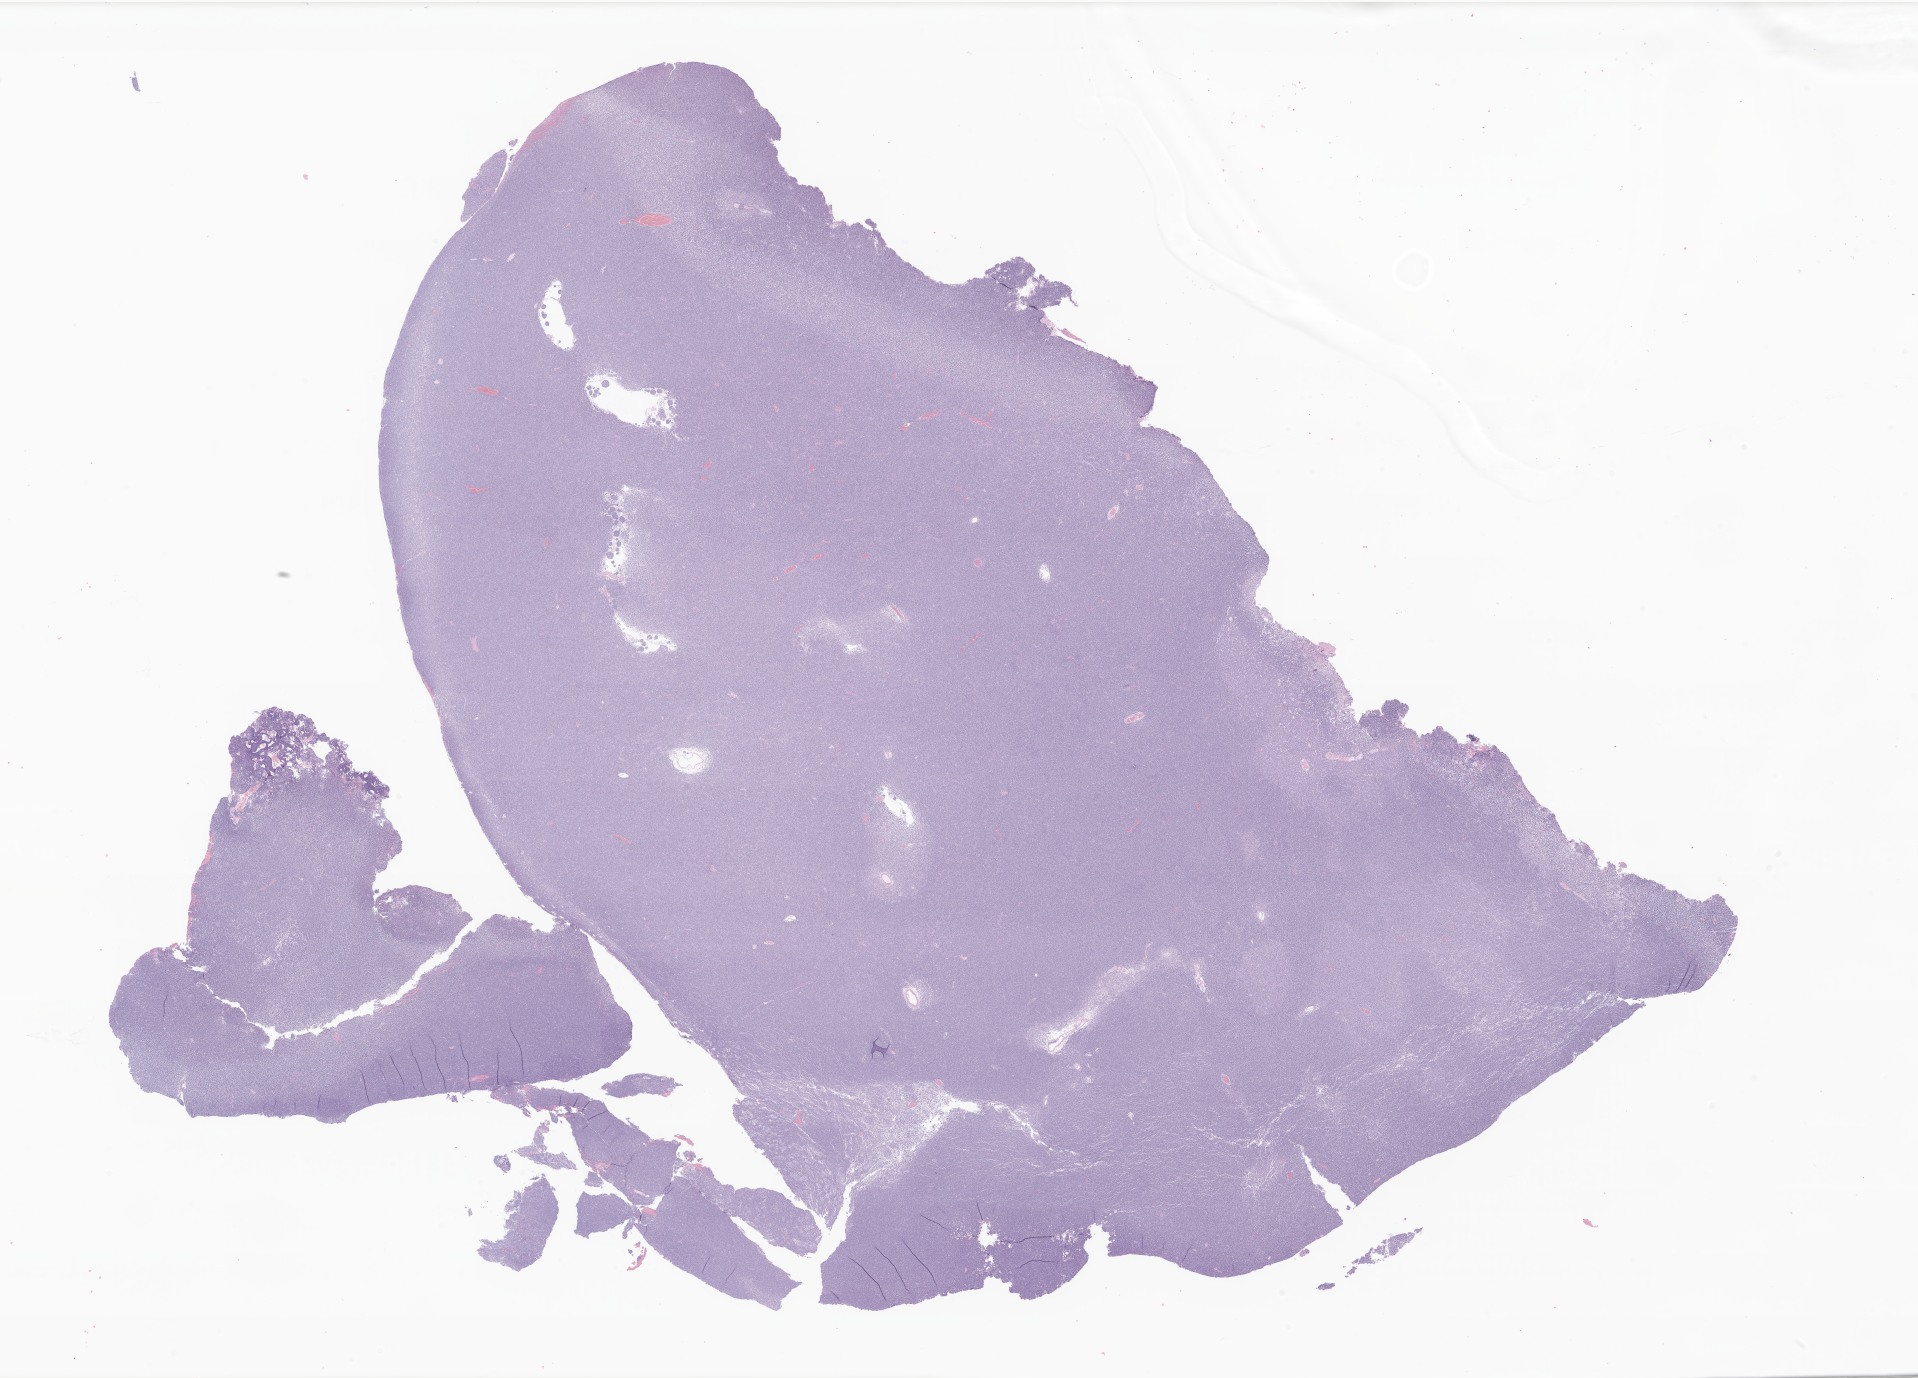
Whole-slide image, haematoxylin and eosin stain of tumor tissue from the brain — whole scanned area (about 32.3 x 23.2 mm) shown as a low-resolution overview; formalin-fixed, paraffin-embedded (FFPE) tissue. Female patient, age 241 months (20 years 1 month).
Recorded diagnosis: Medulloblastoma, NOS.